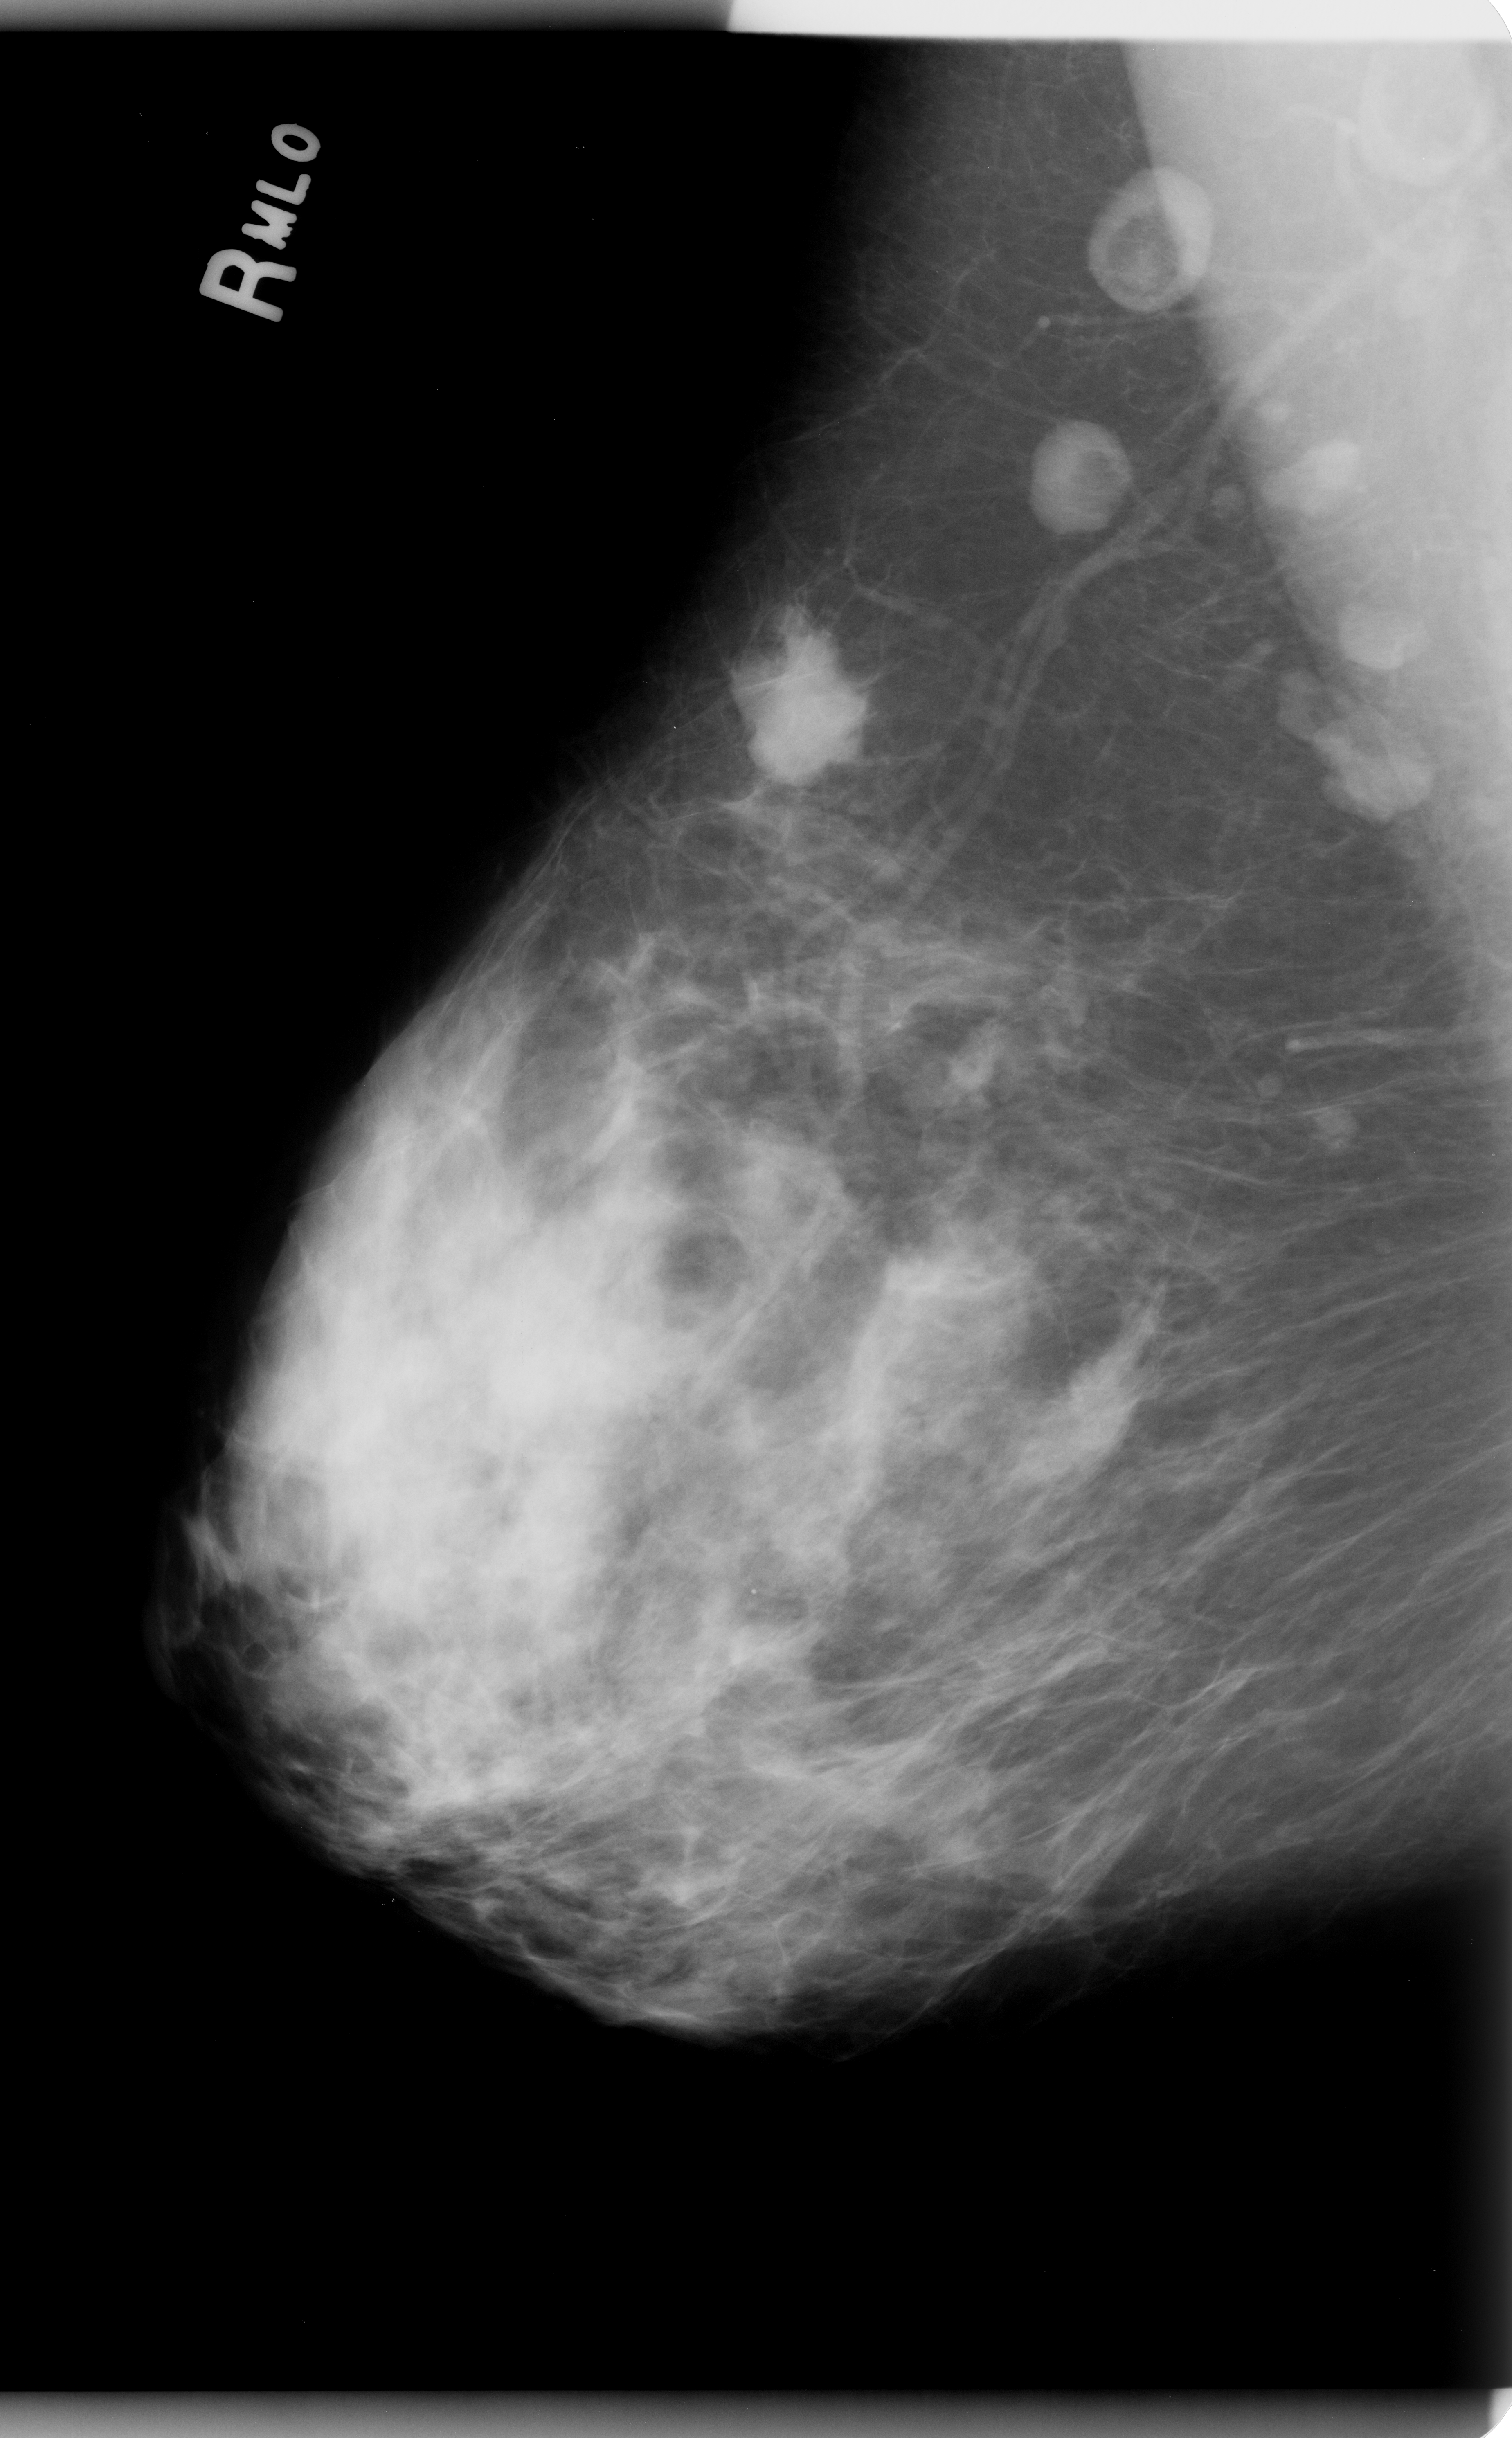
Digitized screen-film mammogram; right breast; MLO view; BI-RADS breast density category 3 (scale 1–4).
- Radiologist-marked abnormalities on this image: mass, shape irregular, margins microlobulated; BI-RADS assessment category 5; pathology (as recorded): malignant.